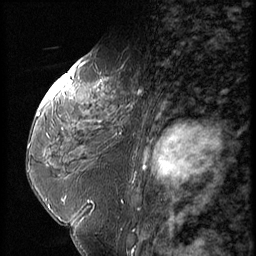
Breast MRI (dynamic contrast-enhanced), one sagittal slice. Slice 33 of 56 in the series (ordered by position). Dynamic contrast-enhanced series, image 2 of 3 at this slice position (ordered by acquisition). 1.5 T. TE 4.2 ms, TR 9 ms. 2.5 mm slice thickness. 256 × 256 image matrix. Patient: female, 59 years. Case-level facts recorded for this patient, not image findings: setting: breast cancer imaged before/during neoadjuvant chemotherapy; receptor status: HER2-positive.
Outlined on this slice (semi-automatic segmentation, software-assisted and operator-edited):
- analysis volume of interest (the breast-tissue region the enhancement analysis was run in; not a lesion): bounding box (x1, y1, x2, y2) in pixels: (44, 66, 151, 135)
- tumour enhancement mask (voxels above the 140 % enhancement threshold inside the analysis volume of interest): (45, 66, 104, 104)